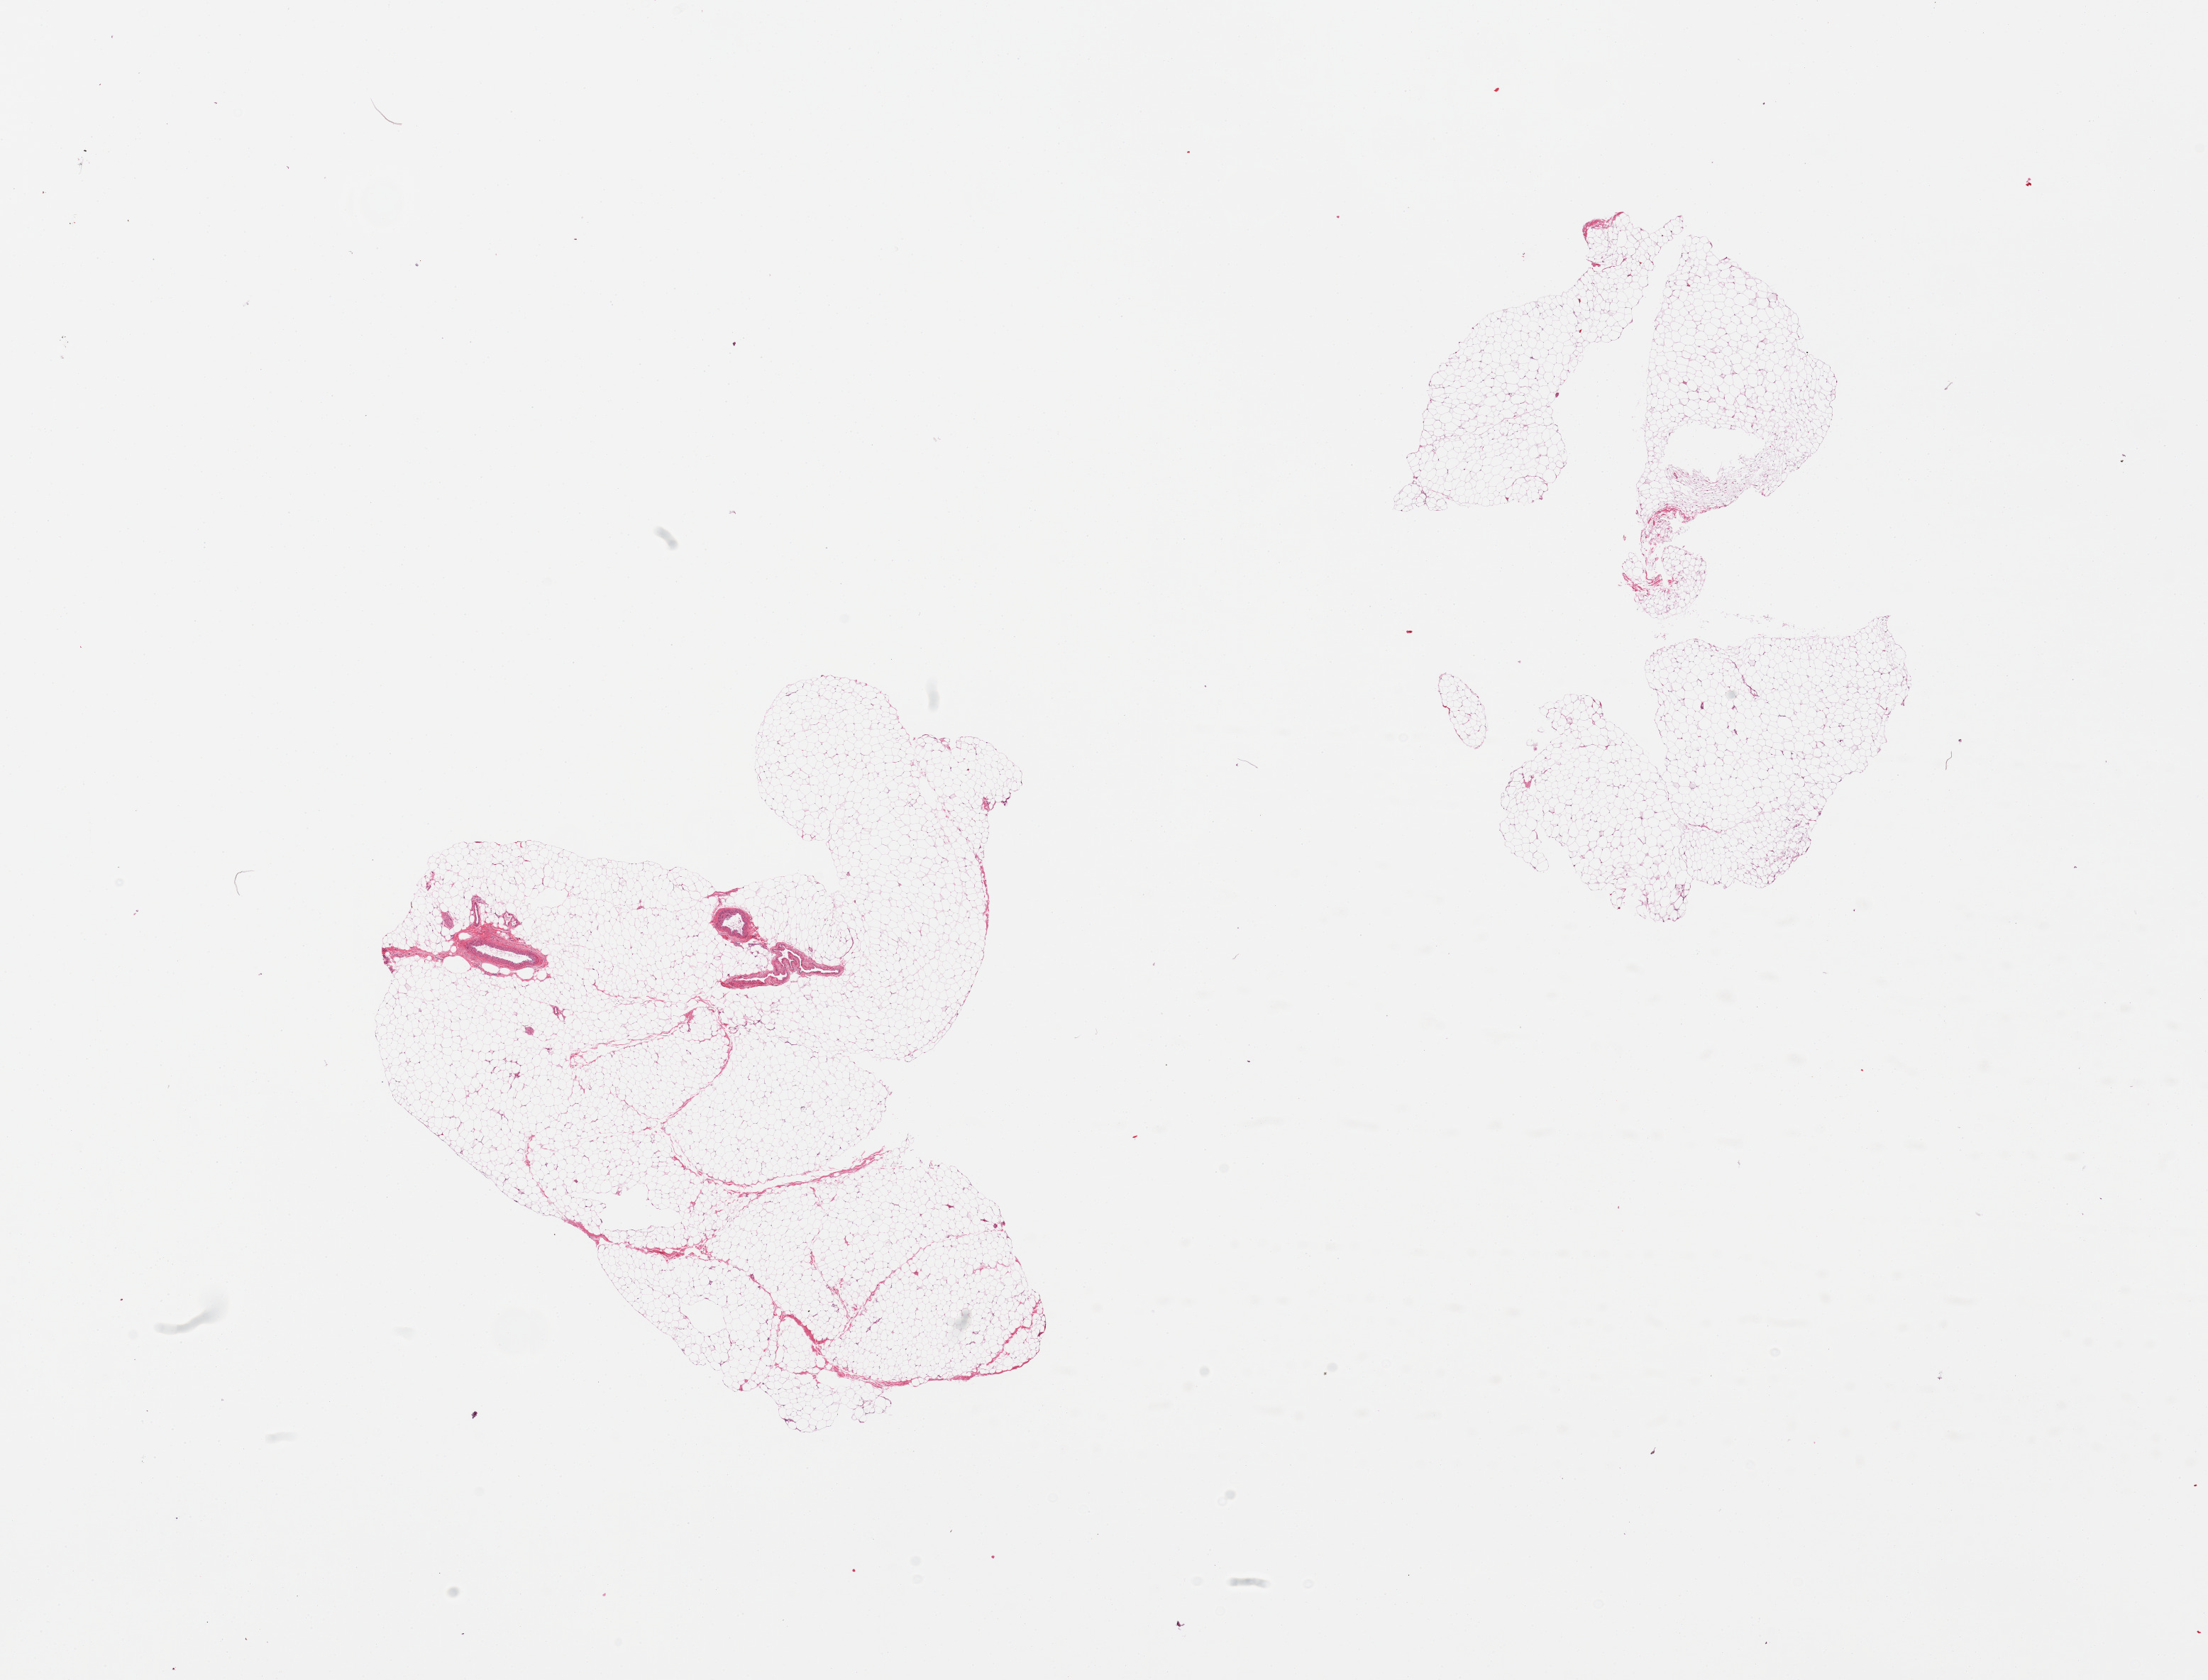
Digitized hematoxylin and eosin (H&E)-stained section — a low-resolution overview of the entire scanned area, about 24.6 x 18.7 mm. PAXgene-fixed, paraffin-embedded tissue. Sampled site (target tissue): breast. Tissue donor sample. Male donor.
Review note (as recorded): 2 pieces, adipose tissue; no ductal elements.